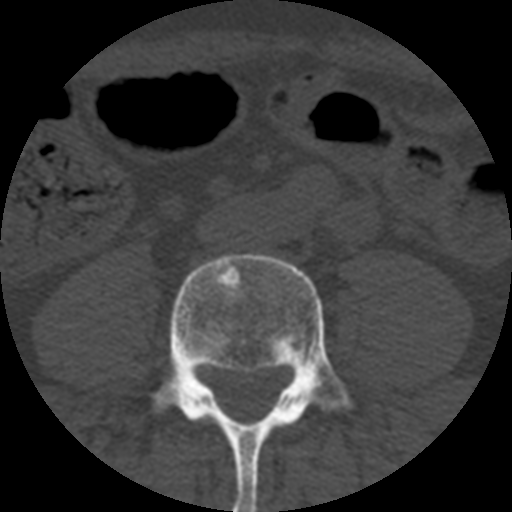
CT including the spine, one axial slice; position 91 of 508 along the scan axis; reconstruction kernel STANDARD; 120 kVp; bone window (W 1800 / L 400 HU); 1.25 mm slice thickness; 512 × 512 image matrix, field of view 160 × 160 mm. Patient age 57 years. Case-level facts recorded for this patient, not image findings: primary cancer: prostate.
Outlined on this slice (semi-automatically segmented with operator editing):
- L4 vertebra: bounding box [x1, y1, x2, y2] px = [152, 254, 354, 512]